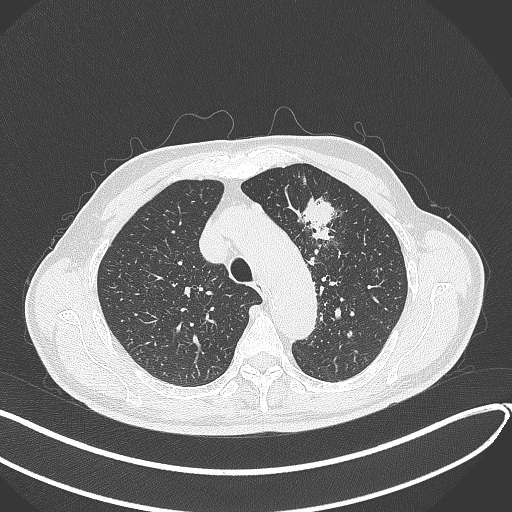
Chest CT, one axial slice. Position 316 of 459 along the scan axis. Reconstruction kernel B70f. 120 kVp. Lung window (W 1500 / L -600 HU). 1 mm slice thickness. 512 × 512 image matrix, field of view 400 × 400 mm. Patient: male, 74 years. From the clinical record (not read from this slice): clinical TNM (as recorded): T2b N0 M1c.
Annotated regions visible in this slice (rectangle marked by the reading radiologist):
- lung tumour (recorded histology: adenocarcinoma): bounding box <298,189,348,250> (left, top, right, bottom; pixels)